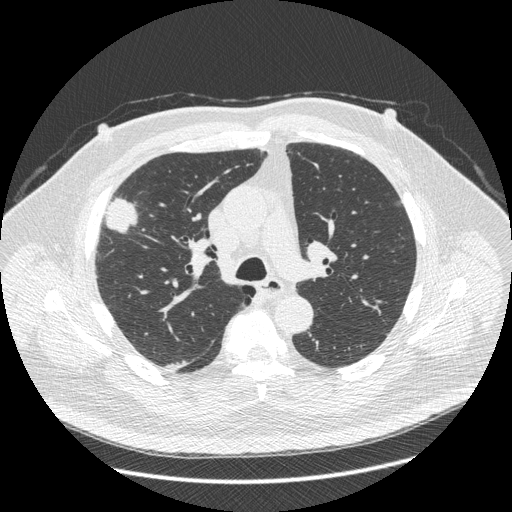
Low-dose screening chest CT, one axial slice; 120 kVp; lung window (W 1500 / L -600 HU); 1.25 mm slice thickness; 512 × 512 image matrix, field of view 400 × 400 mm.
Outlined on this slice (manually delineated by an expert):
- lesion 1 (tumor, upper lobe of right lung): bounding box [x1, y1, x2, y2] px = [106, 198, 137, 232]